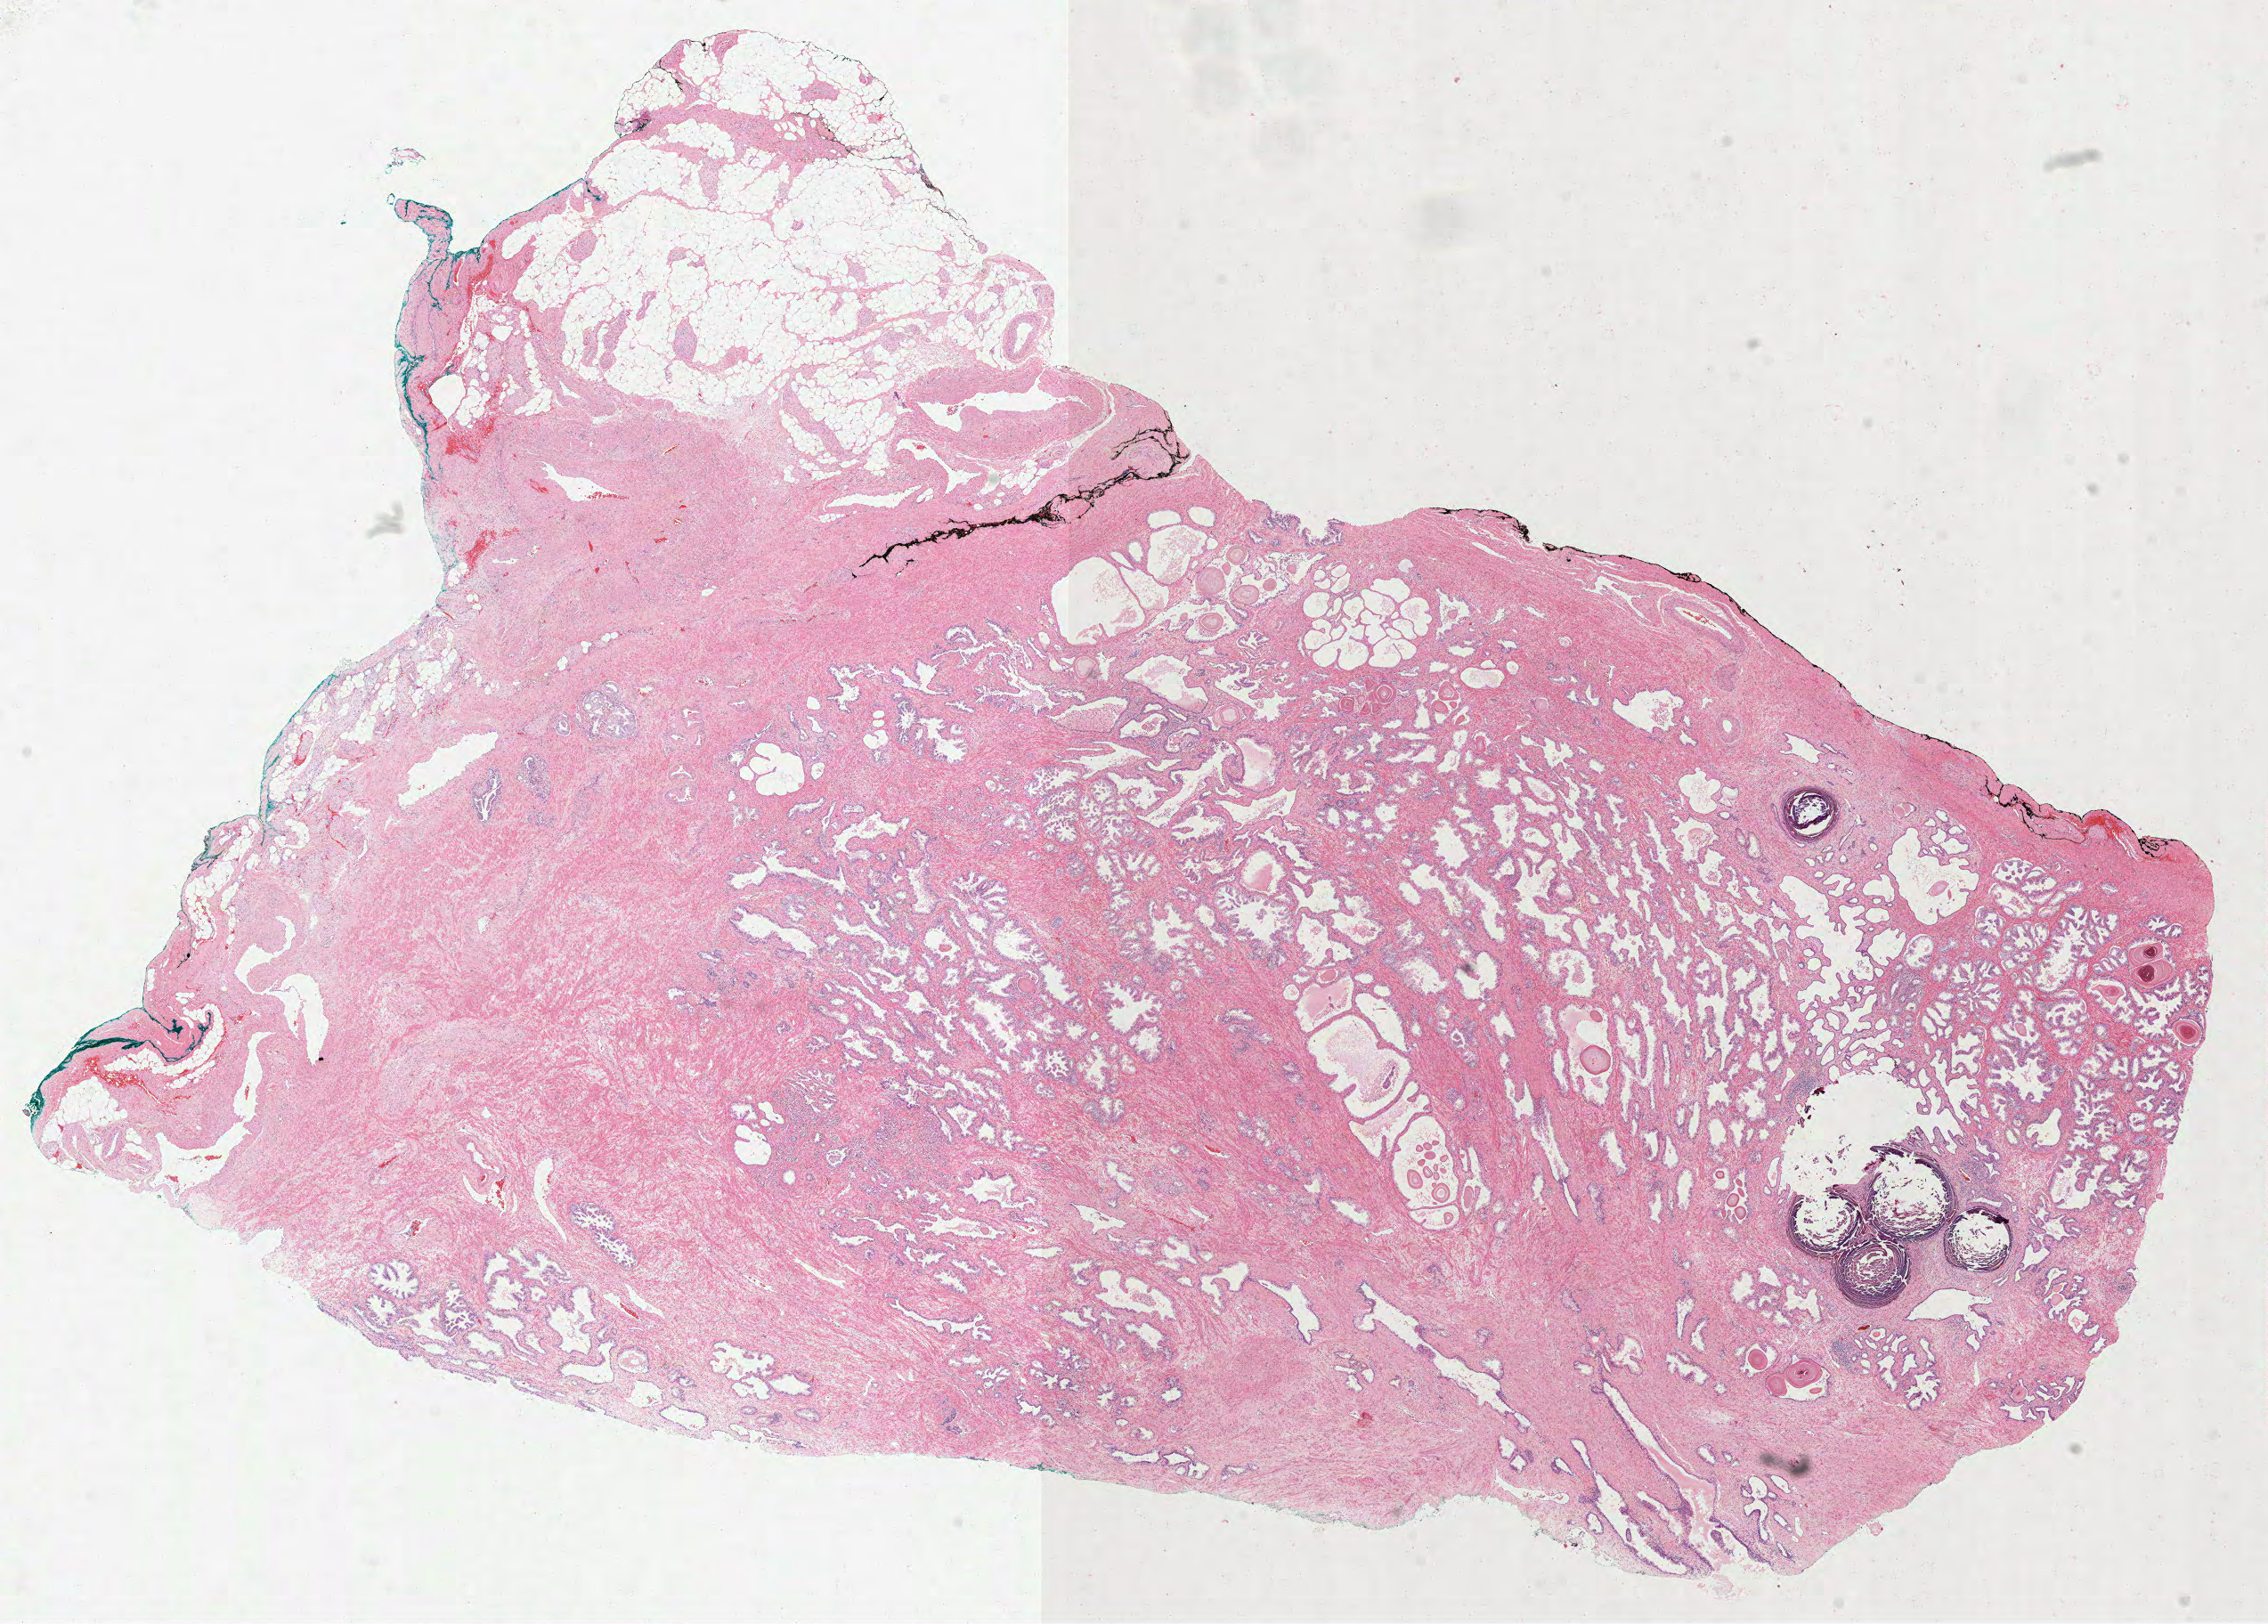
Whole-slide histology image, H&E, whole scanned area (about 20.5 x 14.7 mm, slide scanned at 40x) shown as a low-resolution overview. Formalin-fixed paraffin-embedded (FFPE) diagnostic section. Prostate, primary tumour sample. Patient: male, age at initial diagnosis 66 years. Gleason score: 8 (4+4).
Lymph nodes positive (case pathology): 0 of 10 examined. Diagnosis: Acinar cell carcinoma (prostate gland). Laterality: bilateral.